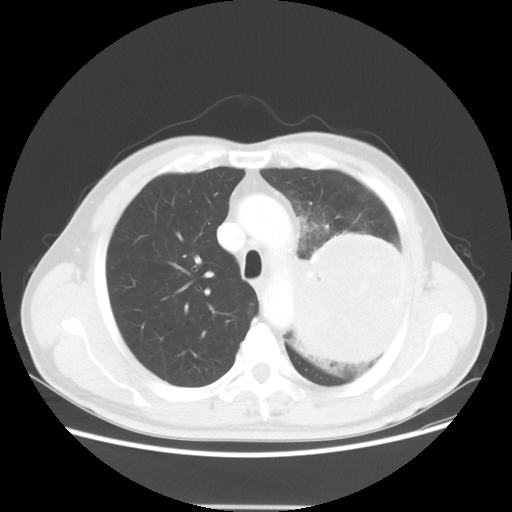
Chest CT, one axial slice; position 39 of 53 along the scan axis; reconstruction kernel STANDARD; lung window (W 1500 / L -600 HU); 5 mm slice thickness; 512 × 512 image matrix, field of view 391 × 391 mm. Male patient, age 60 years. Case-level facts recorded for this patient, not image findings: clinical TNM (as recorded): T4 N1 M1a.
Annotated regions visible in this slice (rectangle marked by the reading radiologist):
- lung tumour (recorded histology: large cell carcinoma): box from (x=279, y=236) to (x=405, y=373) px